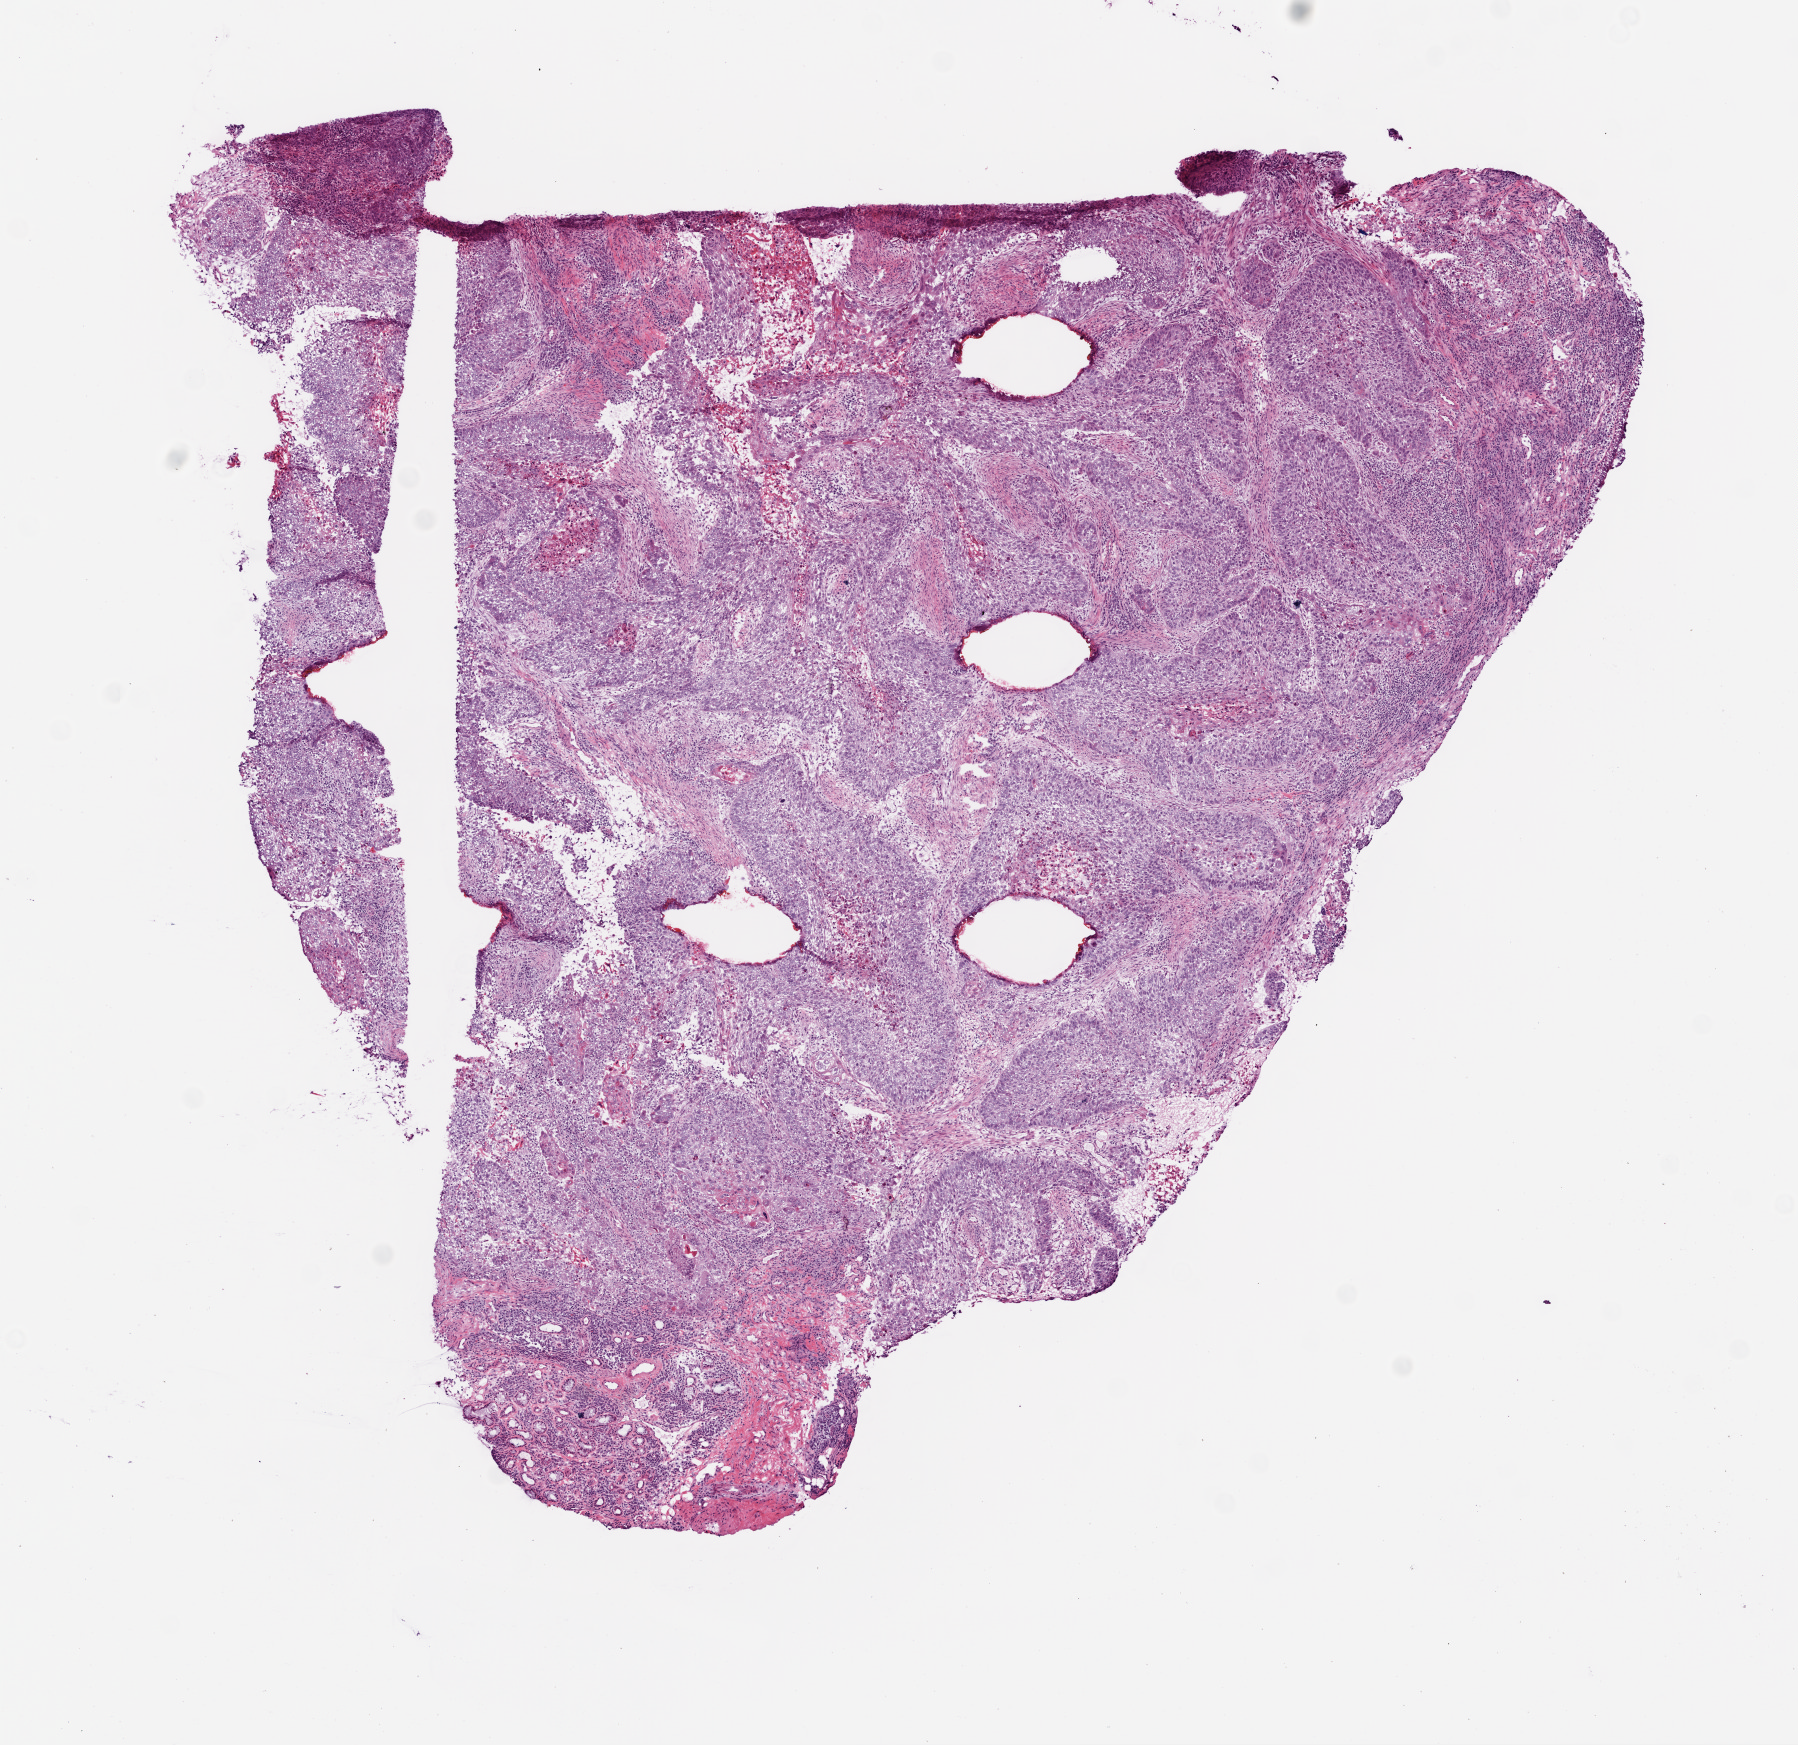
Whole-slide histology image, Hematoxylin and eosin (H&E) stained, low-resolution overview of the scanned area, about 7.3 x 7.0 mm. Frozen section from the top of the tissue portion. Primary tumour sample from the lung. Patient: female, age at initial diagnosis 60 years. Slide review estimates, as recorded: tumour cells 85%, tumour nuclei 70%, normal cells 0%, stromal cells 10%, necrosis 5%.
AJCC pathologic stage: IIA (7th edition). TNM: T1b N1 M0. Pathologic diagnosis: Squamous cell carcinoma, NOS (lower lobe, lung).